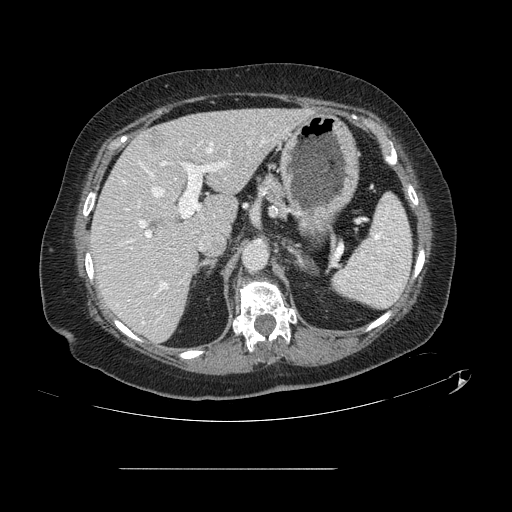
Contrast-enhanced abdominal CT, one axial slice; position 82 of 148 along the scan axis; 120 kVp; soft-tissue window (W 400 / L 40 HU); 2.5 mm slice thickness; 512 × 512 image matrix, field of view 439 × 439 mm. Female patient, age 75 years. Case-level facts recorded for this patient, not image findings: diagnosis: colorectal cancer liver metastases, imaged before liver resection; multiple liver metastases: no; largest metastasis: 2.4 cm; disease in both lobes: no.
Annotated regions visible in this slice (outlined manually by an expert reader):
- hepatic veins: bounding box (x1, y1, x2, y2) in pixels: (153, 144, 212, 197)
- liver: (91, 109, 307, 342)
- planned liver remnant (the part of the liver to remain after resection): (91, 109, 308, 342)
- portal vein (with intrahepatic branches): (131, 133, 266, 291)
- liver metastasis: (149, 133, 160, 148)